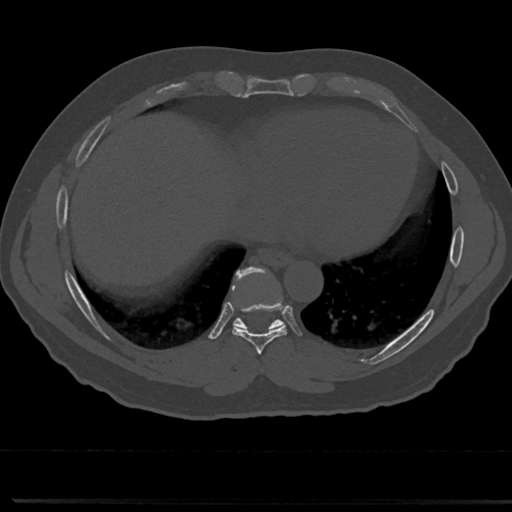
CT including the spine, one axial slice. Slice 339 of 817 in the series (ordered by position). 120 kVp. Bone window (W 1800 / L 400 HU). 0.5 mm slice thickness. 512 × 512 image matrix. Patient: male, 61 years. Case-level facts recorded for this patient, not image findings: primary cancer: prostate.
Outlined on this slice (semi-automatically segmented with operator editing):
- T7 vertebra: bounding box (x1, y1, x2, y2) in pixels: (258, 344, 266, 377)
- T8 vertebra: (213, 271, 308, 355)